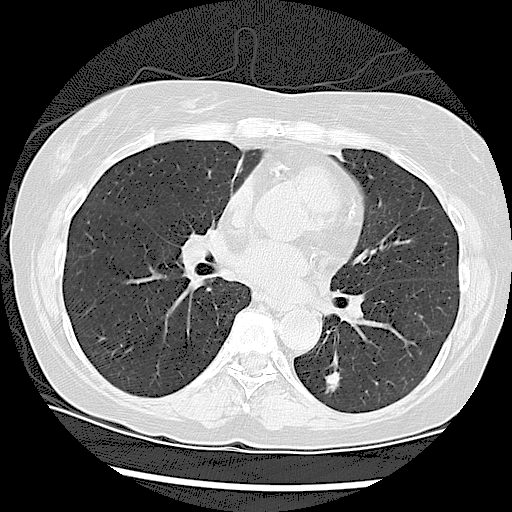
Low-dose screening chest CT, one axial slice. Position 51 of 108 along the scan axis. Lung window (W 1500 / L -600 HU). 2.5 mm slice thickness. 512 × 512 image matrix, field of view 330 × 330 mm.
Outlined on this slice (outlined manually by an expert reader):
- lesion 1 (tumor, lower lobe of left lung): bounding box <325,370,342,394> (left, top, right, bottom; pixels)